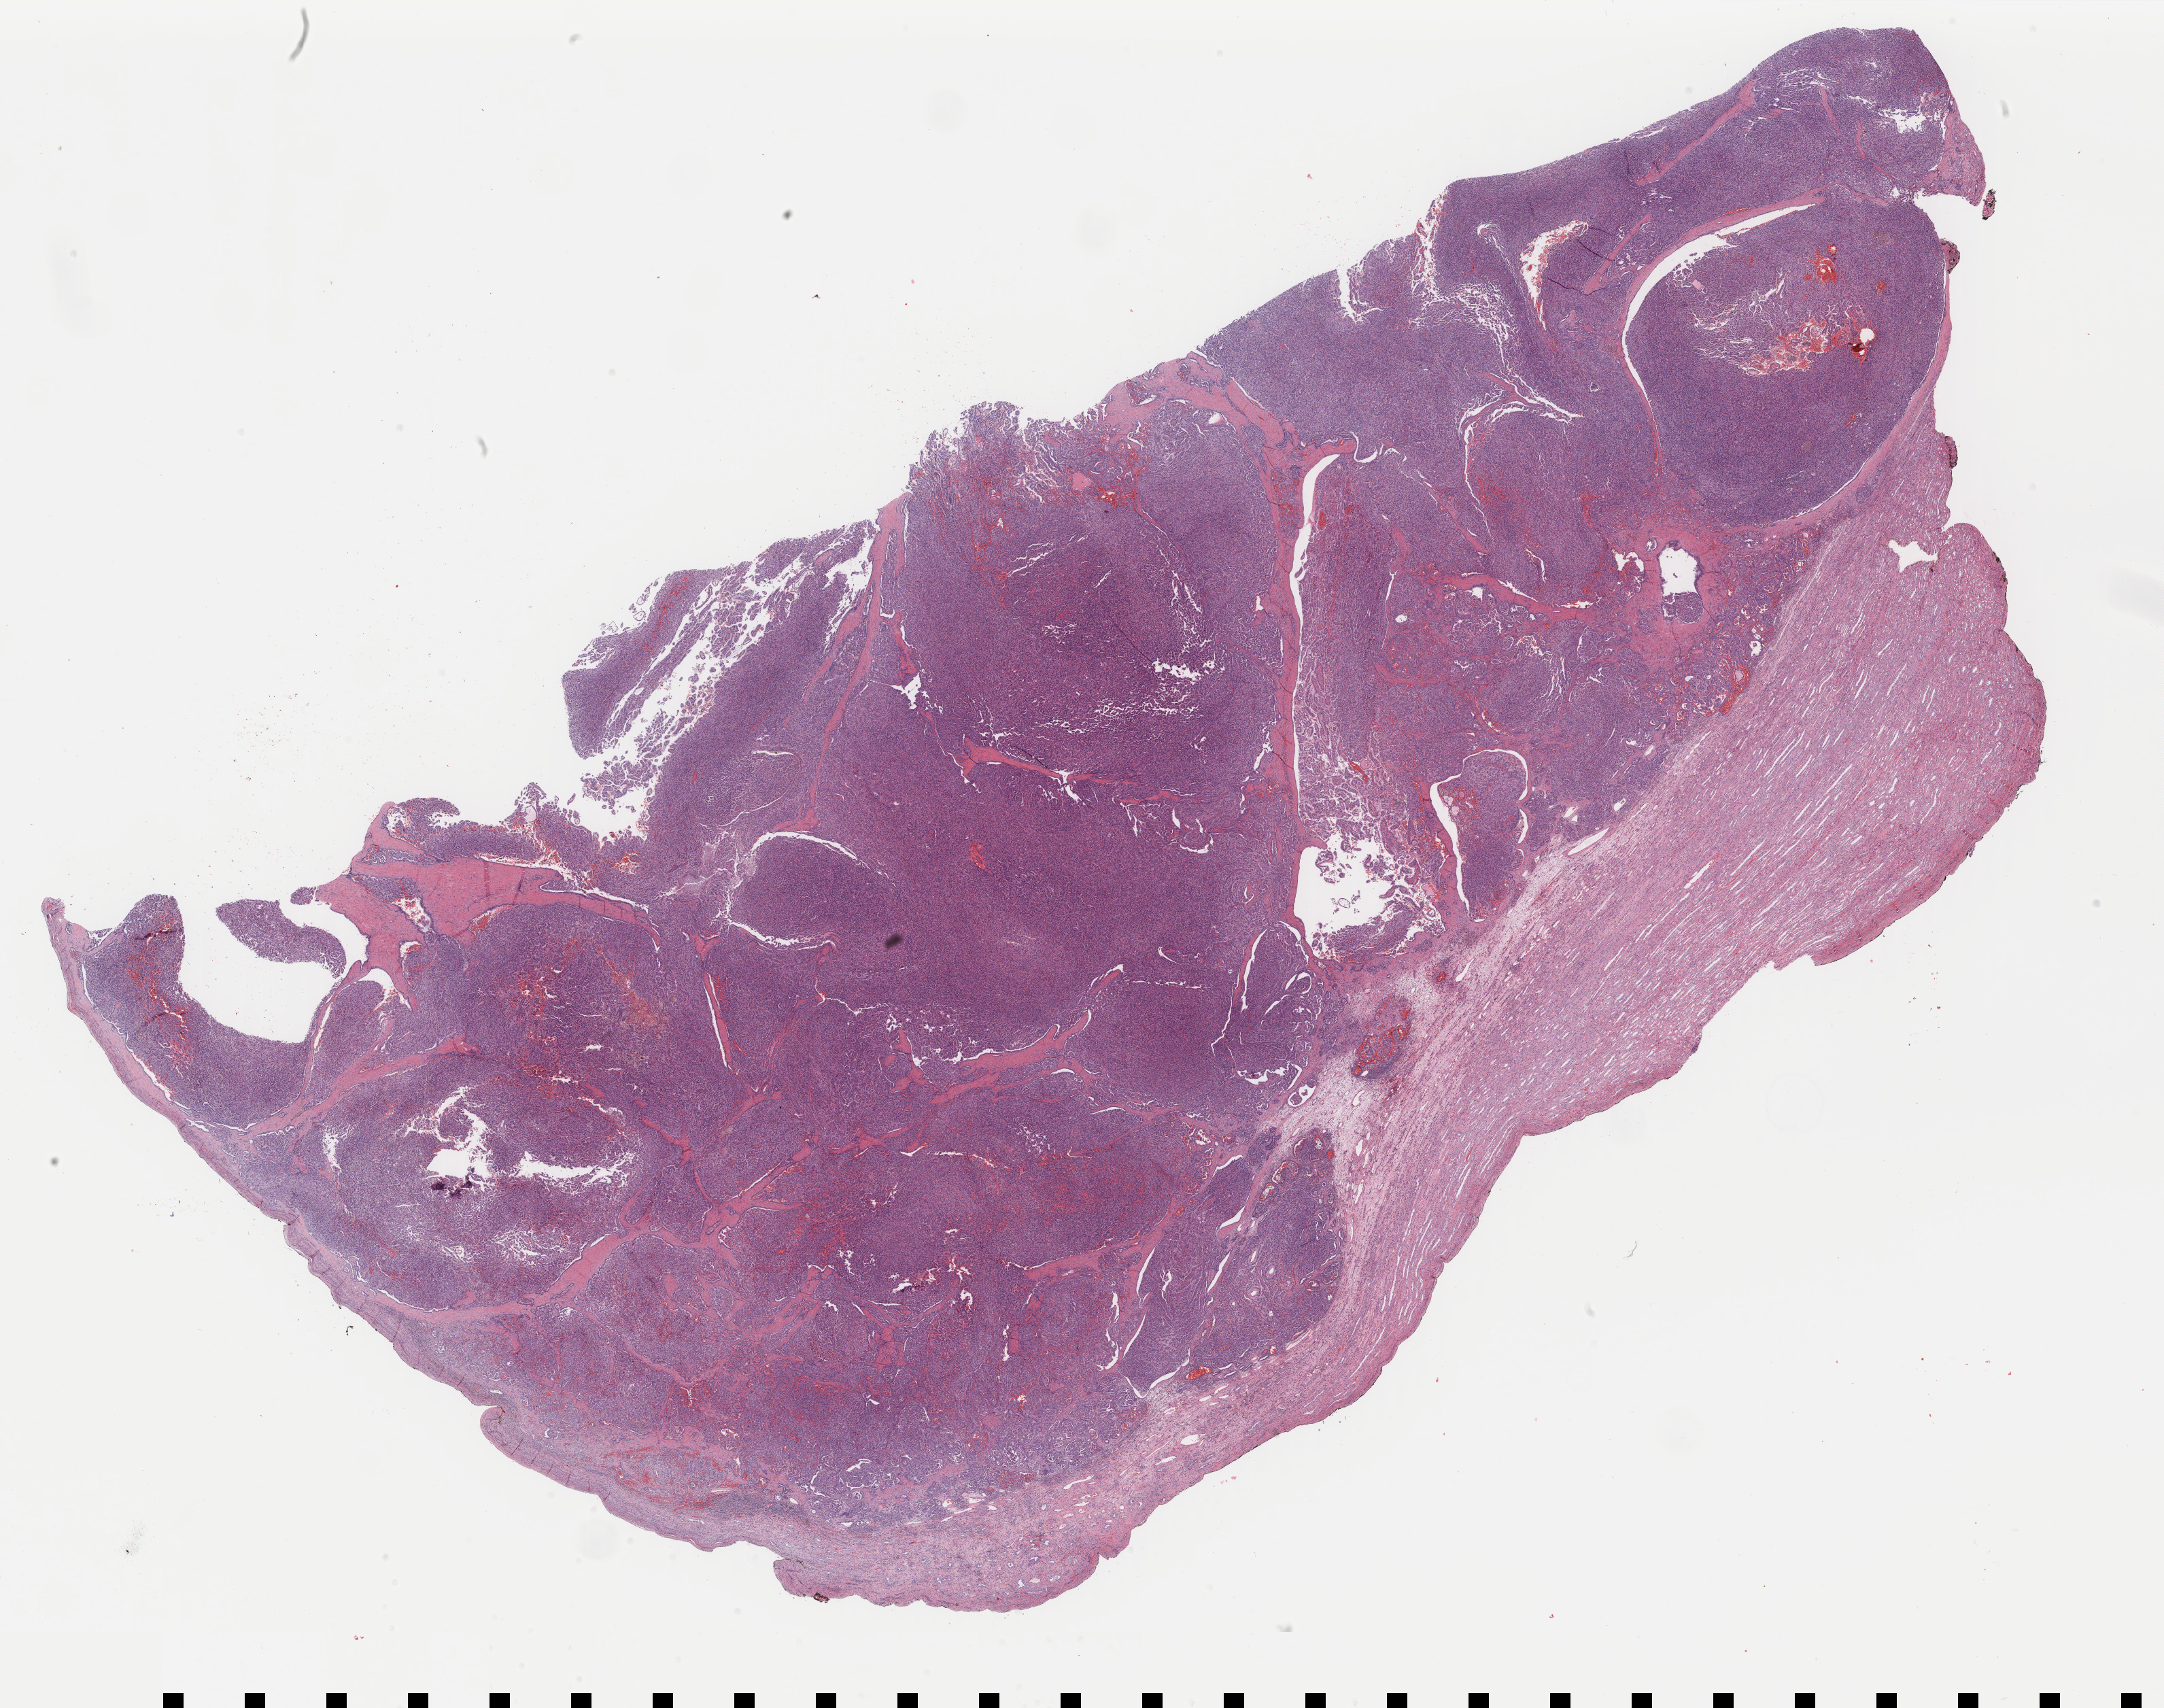
Whole-slide histology image, H&E — whole scanned area (about 25.3 x 19.9 mm, slide scanned at 40x) shown as a low-resolution overview, formalin-fixed paraffin-embedded (FFPE) diagnostic section, primary tumour sample from the kidney. Male, age 40 years at initial diagnosis.
TNM: T1a NX MX. Laterality: right. Diagnosis: Papillary adenocarcinoma, NOS. AJCC pathologic stage: I (7th edition).